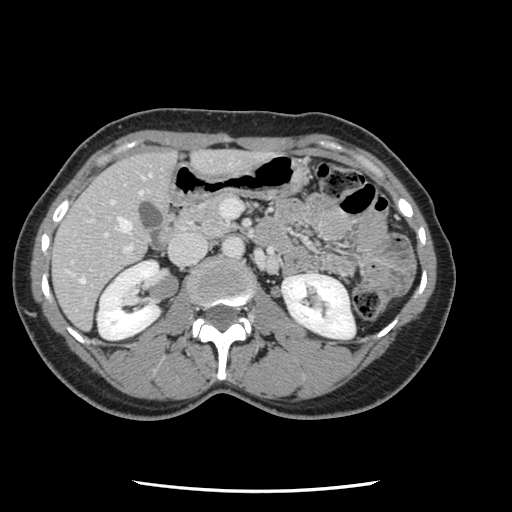
Contrast-enhanced abdominal CT, one axial slice; position 48 of 134 along the scan axis; 120 kVp; intravenous contrast given; soft-tissue window (W 400 / L 40 HU); 512 × 512 image matrix. Female patient, age 43 years. From the clinical record (not read from this slice): diagnosis: colorectal cancer liver metastases, imaged before liver resection; multiple liver metastases: yes; largest metastasis: 3.4 cm; disease in both lobes: yes.
Outlined on this slice (outlined manually by an expert reader):
- hepatic veins: bounding box [x1, y1, x2, y2] px = [80, 174, 151, 283]
- liver: [53, 152, 260, 328]
- planned liver remnant (the part of the liver to remain after resection): [53, 152, 175, 328]
- portal vein (with intrahepatic branches): [71, 201, 241, 302]